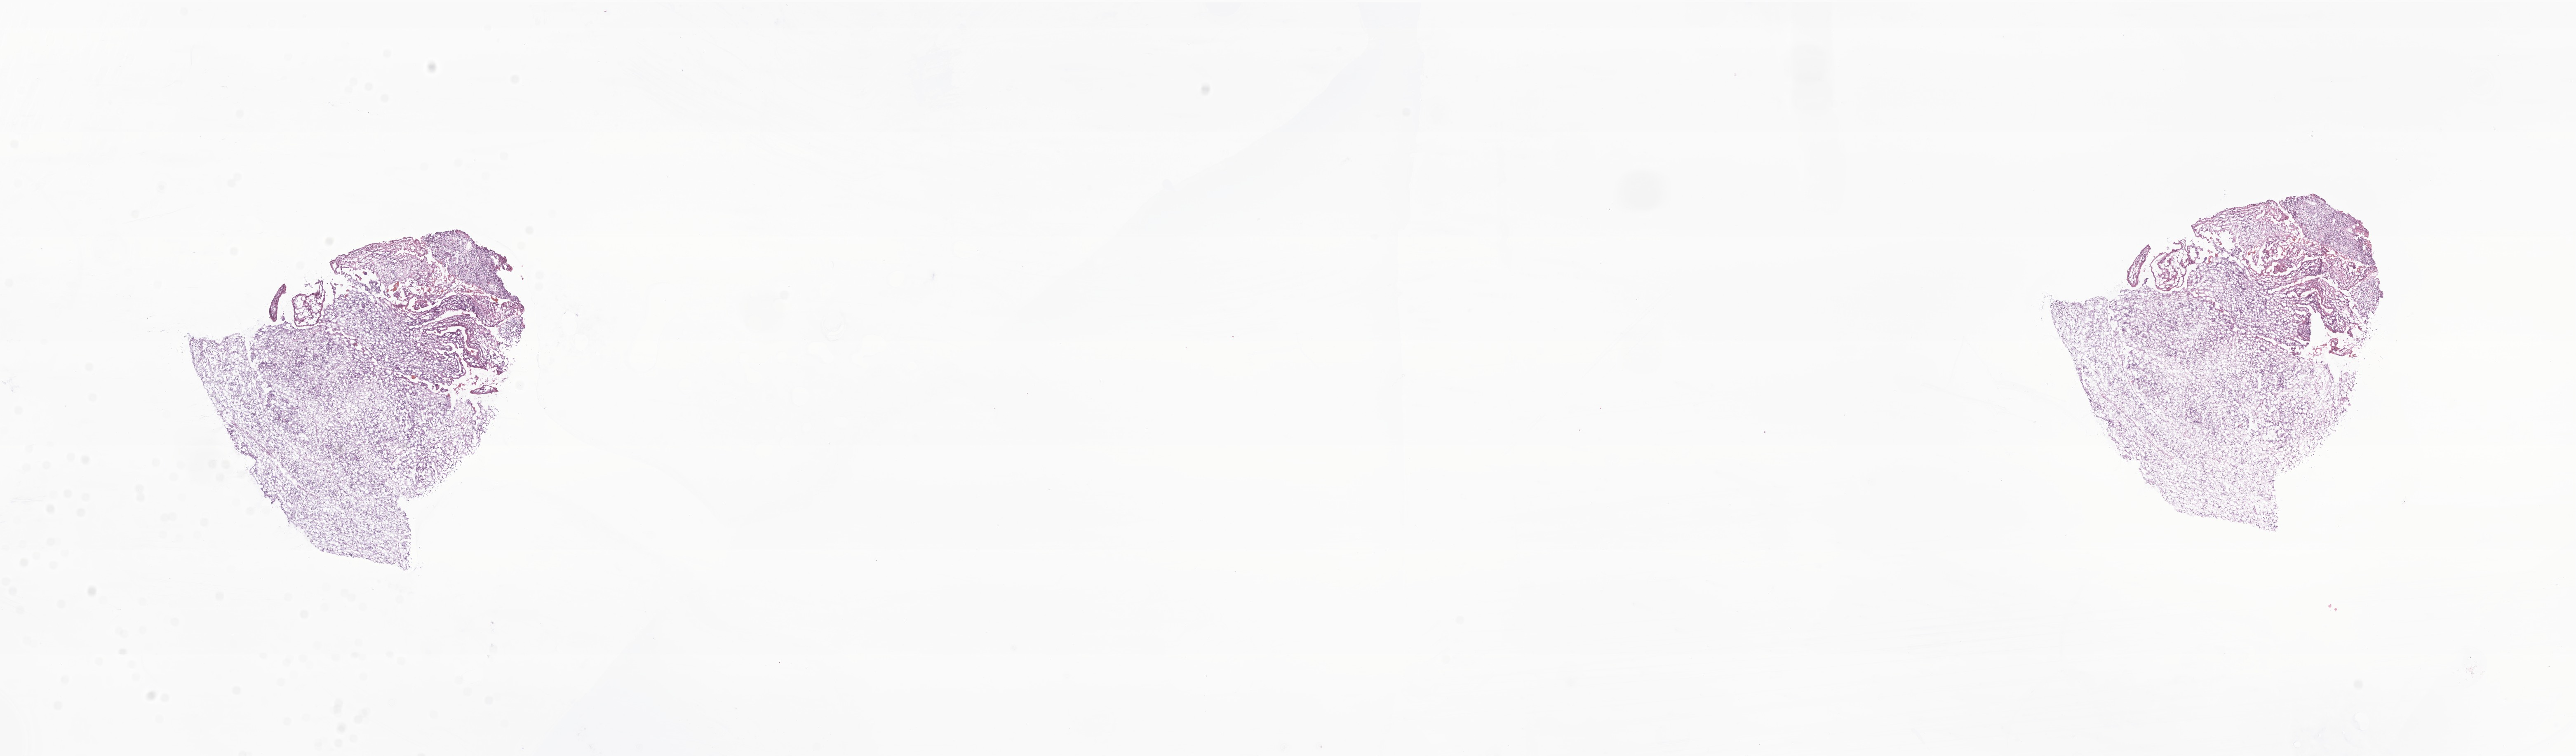
Digitized H&E-stained section of tumor tissue from the anus — a low-resolution overview of the entire scanned area, about 26.3 x 7.7 mm; frozen section. Patient: male, age 115 months (9 years 7 months).
Diagnosis: Rhabdomyosarcoma, NOS.